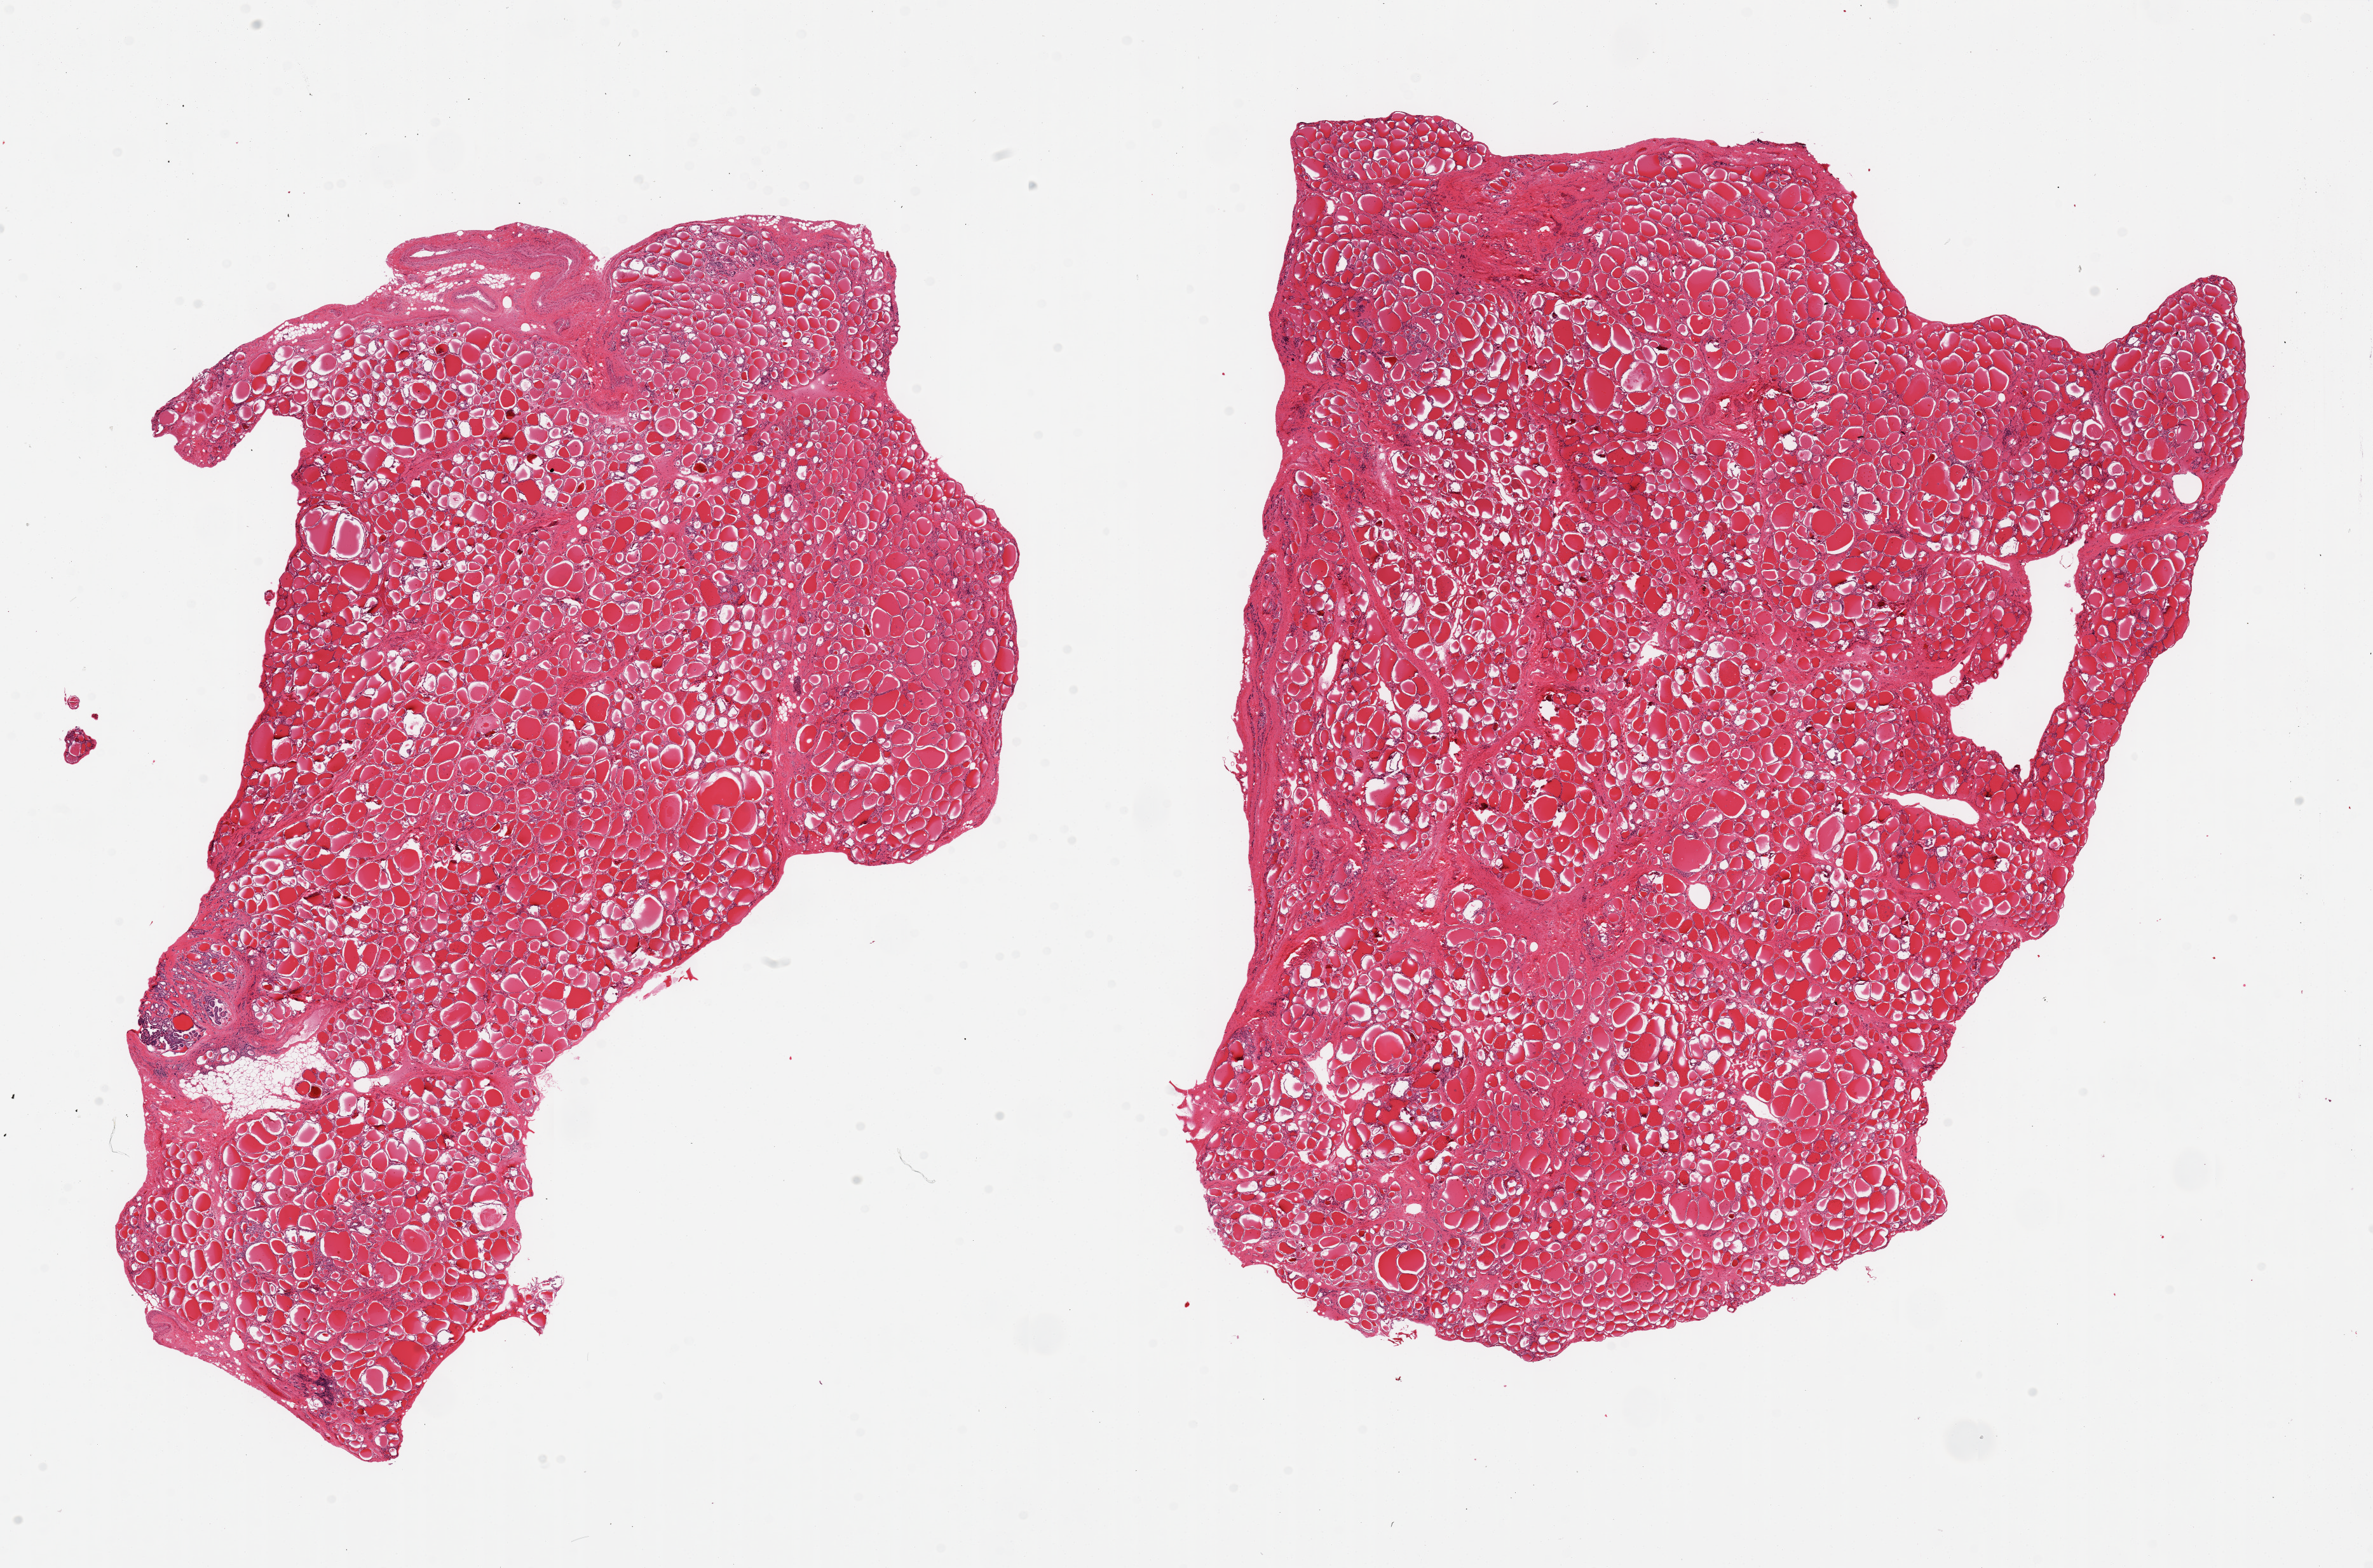
Digitized haematoxylin and eosin-stained section, shown as a low-resolution overview of the whole scanned area (about 29.5 x 19.5 mm, slide scanned at 20x). PAXgene-fixed paraffin-embedded (PFPE) section. Section of thyroid (target tissue). Donor tissue sample. Donor sex: male.
Review note (as recorded): 2 pieces, no abnormalities.